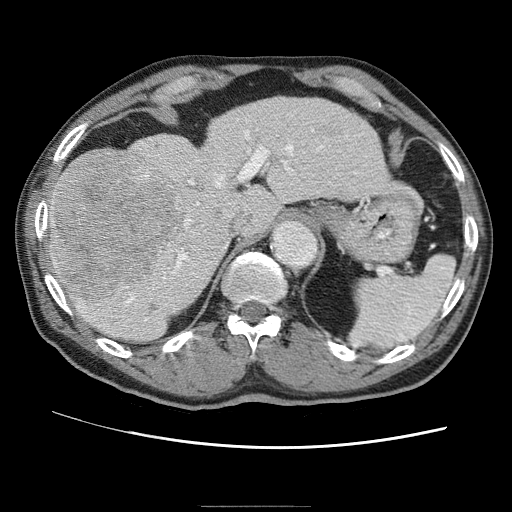
Contrast-enhanced abdominal CT (liver protocol), one axial slice; slice 41 of 75 in the series (ordered by position); 120 kVp; one of 2 acquisitions stored at this slice position; soft-tissue window (W 400 / L 40 HU); 512 × 512 image matrix, field of view 360 × 360 mm. From the clinical record (not read from this slice): diagnosis: hepatocellular carcinoma (patient treated with transarterial chemoembolisation; whether this scan precedes or follows treatment is not stated here); TNM stage (as recorded): Stage-II; Child-Pugh class: A; tumour differentiation: well differentiated; tumour nodularity: multinodular.
Outlined on this slice (semi-automatic segmentation, software-assisted and operator-edited):
- liver parenchyma outside the tumour (the mass and vessels are separate outlines, so this box may not span the whole liver): bounding box [x1, y1, x2, y2] px = [48, 98, 394, 342]
- mass: [49, 152, 178, 296]
- liver vessels: [83, 136, 298, 310]